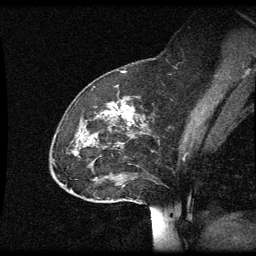
Breast MRI (dynamic contrast-enhanced), one sagittal slice. Slice 21 of 60 in the series (ordered by position). Dynamic contrast-enhanced series, image 2 of 3 at this slice position (ordered by acquisition). 1.5 T. TE 4.2 ms, TR 8.9 ms. 256 × 256 image matrix. Female patient, age 49 years. From the clinical record (not read from this slice): setting: breast cancer imaged before/during neoadjuvant chemotherapy; receptor status: HR-positive, HER2-negative.
Structures marked on this image (semi-automatically segmented with operator editing):
- analysis volume of interest (the breast-tissue region the enhancement analysis was run in; not a lesion): bounding box [x1, y1, x2, y2] px = [51, 98, 146, 205]
- tumour enhancement mask (voxels above the 70 % enhancement threshold inside the analysis volume of interest): [106, 112, 131, 125]